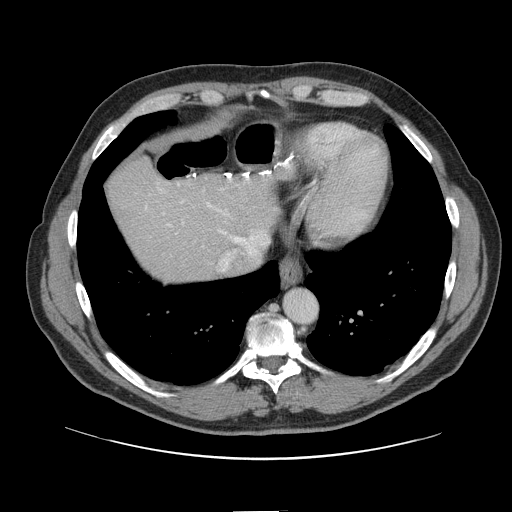
Contrast-enhanced abdominal CT, one axial slice; position 129 of 161 along the scan axis; intravenous contrast given; soft-tissue window (W 400 / L 40 HU); 2.5 mm slice thickness; 512 × 512 image matrix, field of view 412 × 412 mm. Male patient, age 66 years. Case-level facts recorded for this patient, not image findings: diagnosis: colorectal cancer liver metastases, imaged before liver resection; multiple liver metastases: no; largest metastasis: 3.5 cm; chemotherapy before resection: yes.
Annotated regions visible in this slice (outlined manually by an expert reader):
- hepatic veins: bounding box [x1, y1, x2, y2] px = [146, 179, 269, 272]
- liver: [108, 158, 277, 283]
- planned liver remnant (the part of the liver to remain after resection): [108, 159, 277, 282]